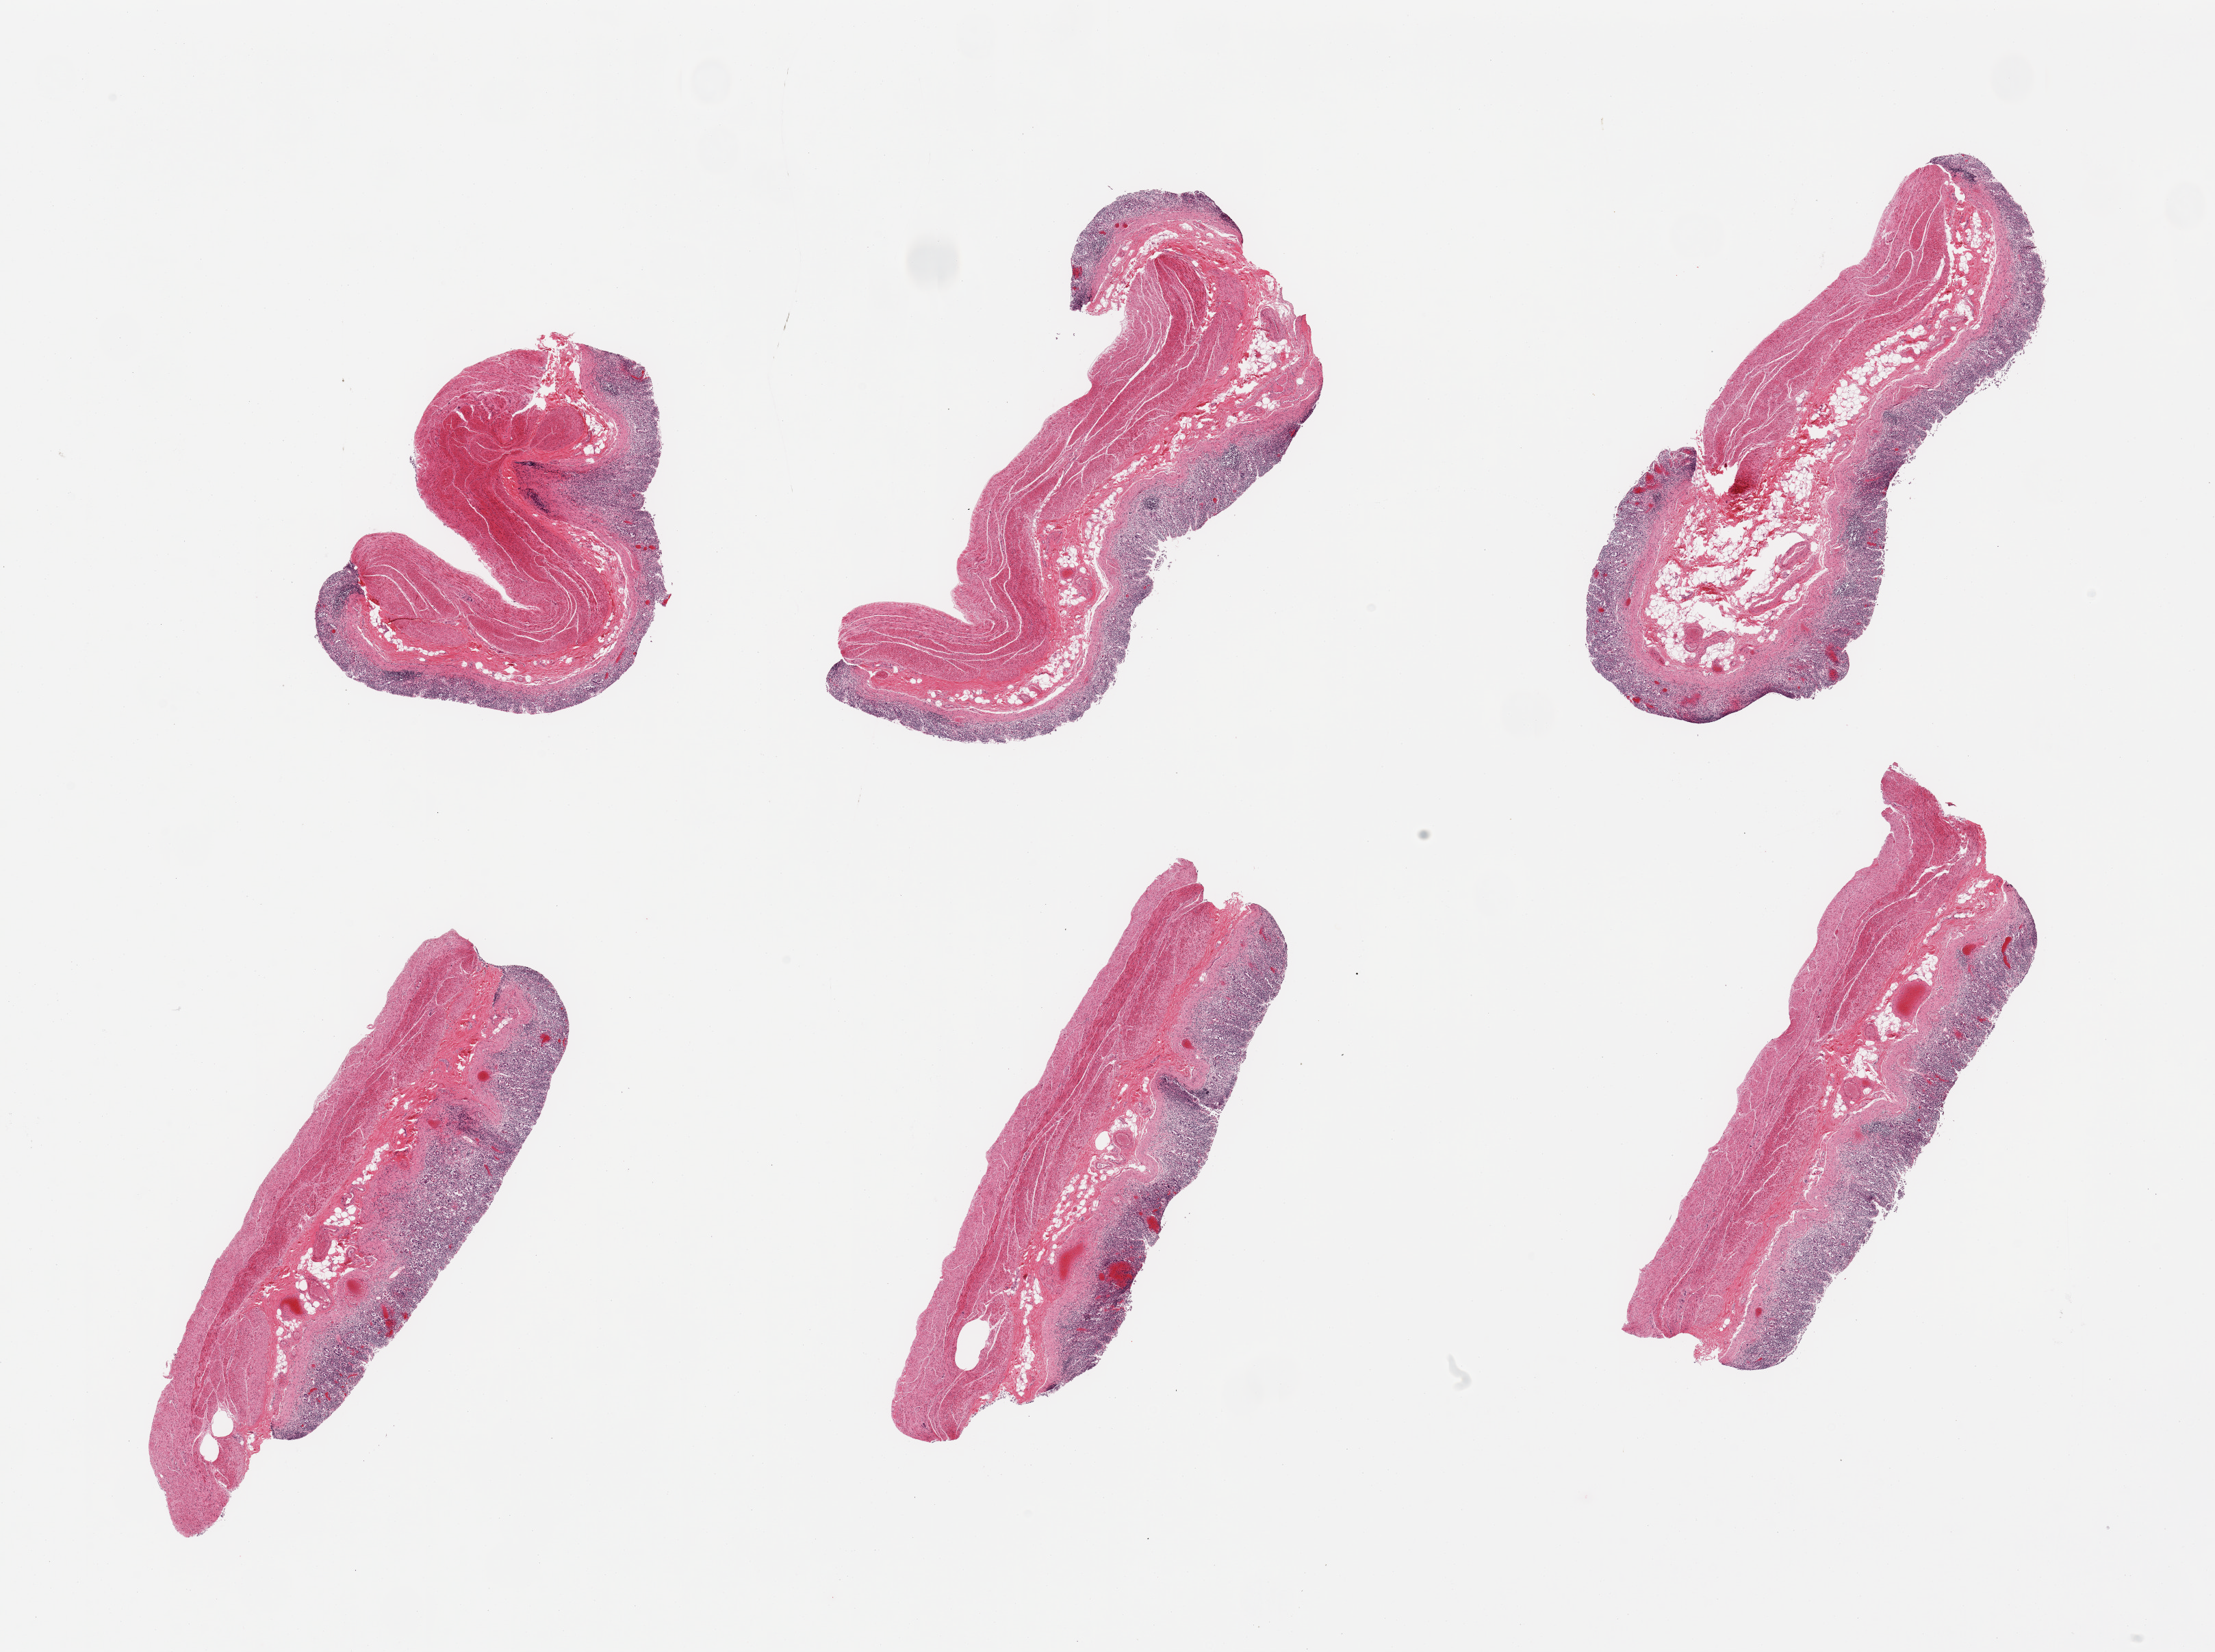
Whole-slide image, haematoxylin and eosin stain — whole scanned area (about 25.6 x 19.1 mm) shown as a low-resolution overview; PAXgene-fixed, paraffin-embedded tissue; sampled site (target tissue): stomach; donor tissue sample. Donor sex: male.
Pathologist's review note for this sample: 6 pieces, mucosa markedly autolyzed.